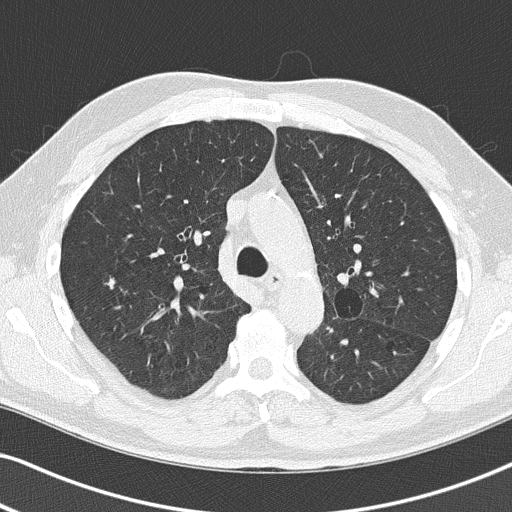
Low-dose screening chest CT, one axial slice; slice 92 of 140 in the series (ordered by position); lung window (W 1500 / L -600 HU); 2 mm slice thickness; 512 × 512 image matrix, field of view 330 × 330 mm.
Annotated regions visible in this slice (expert manual segmentation):
- lesion 1 (tumor, upper lobe of right lung): box from (x=108, y=280) to (x=115, y=288) px